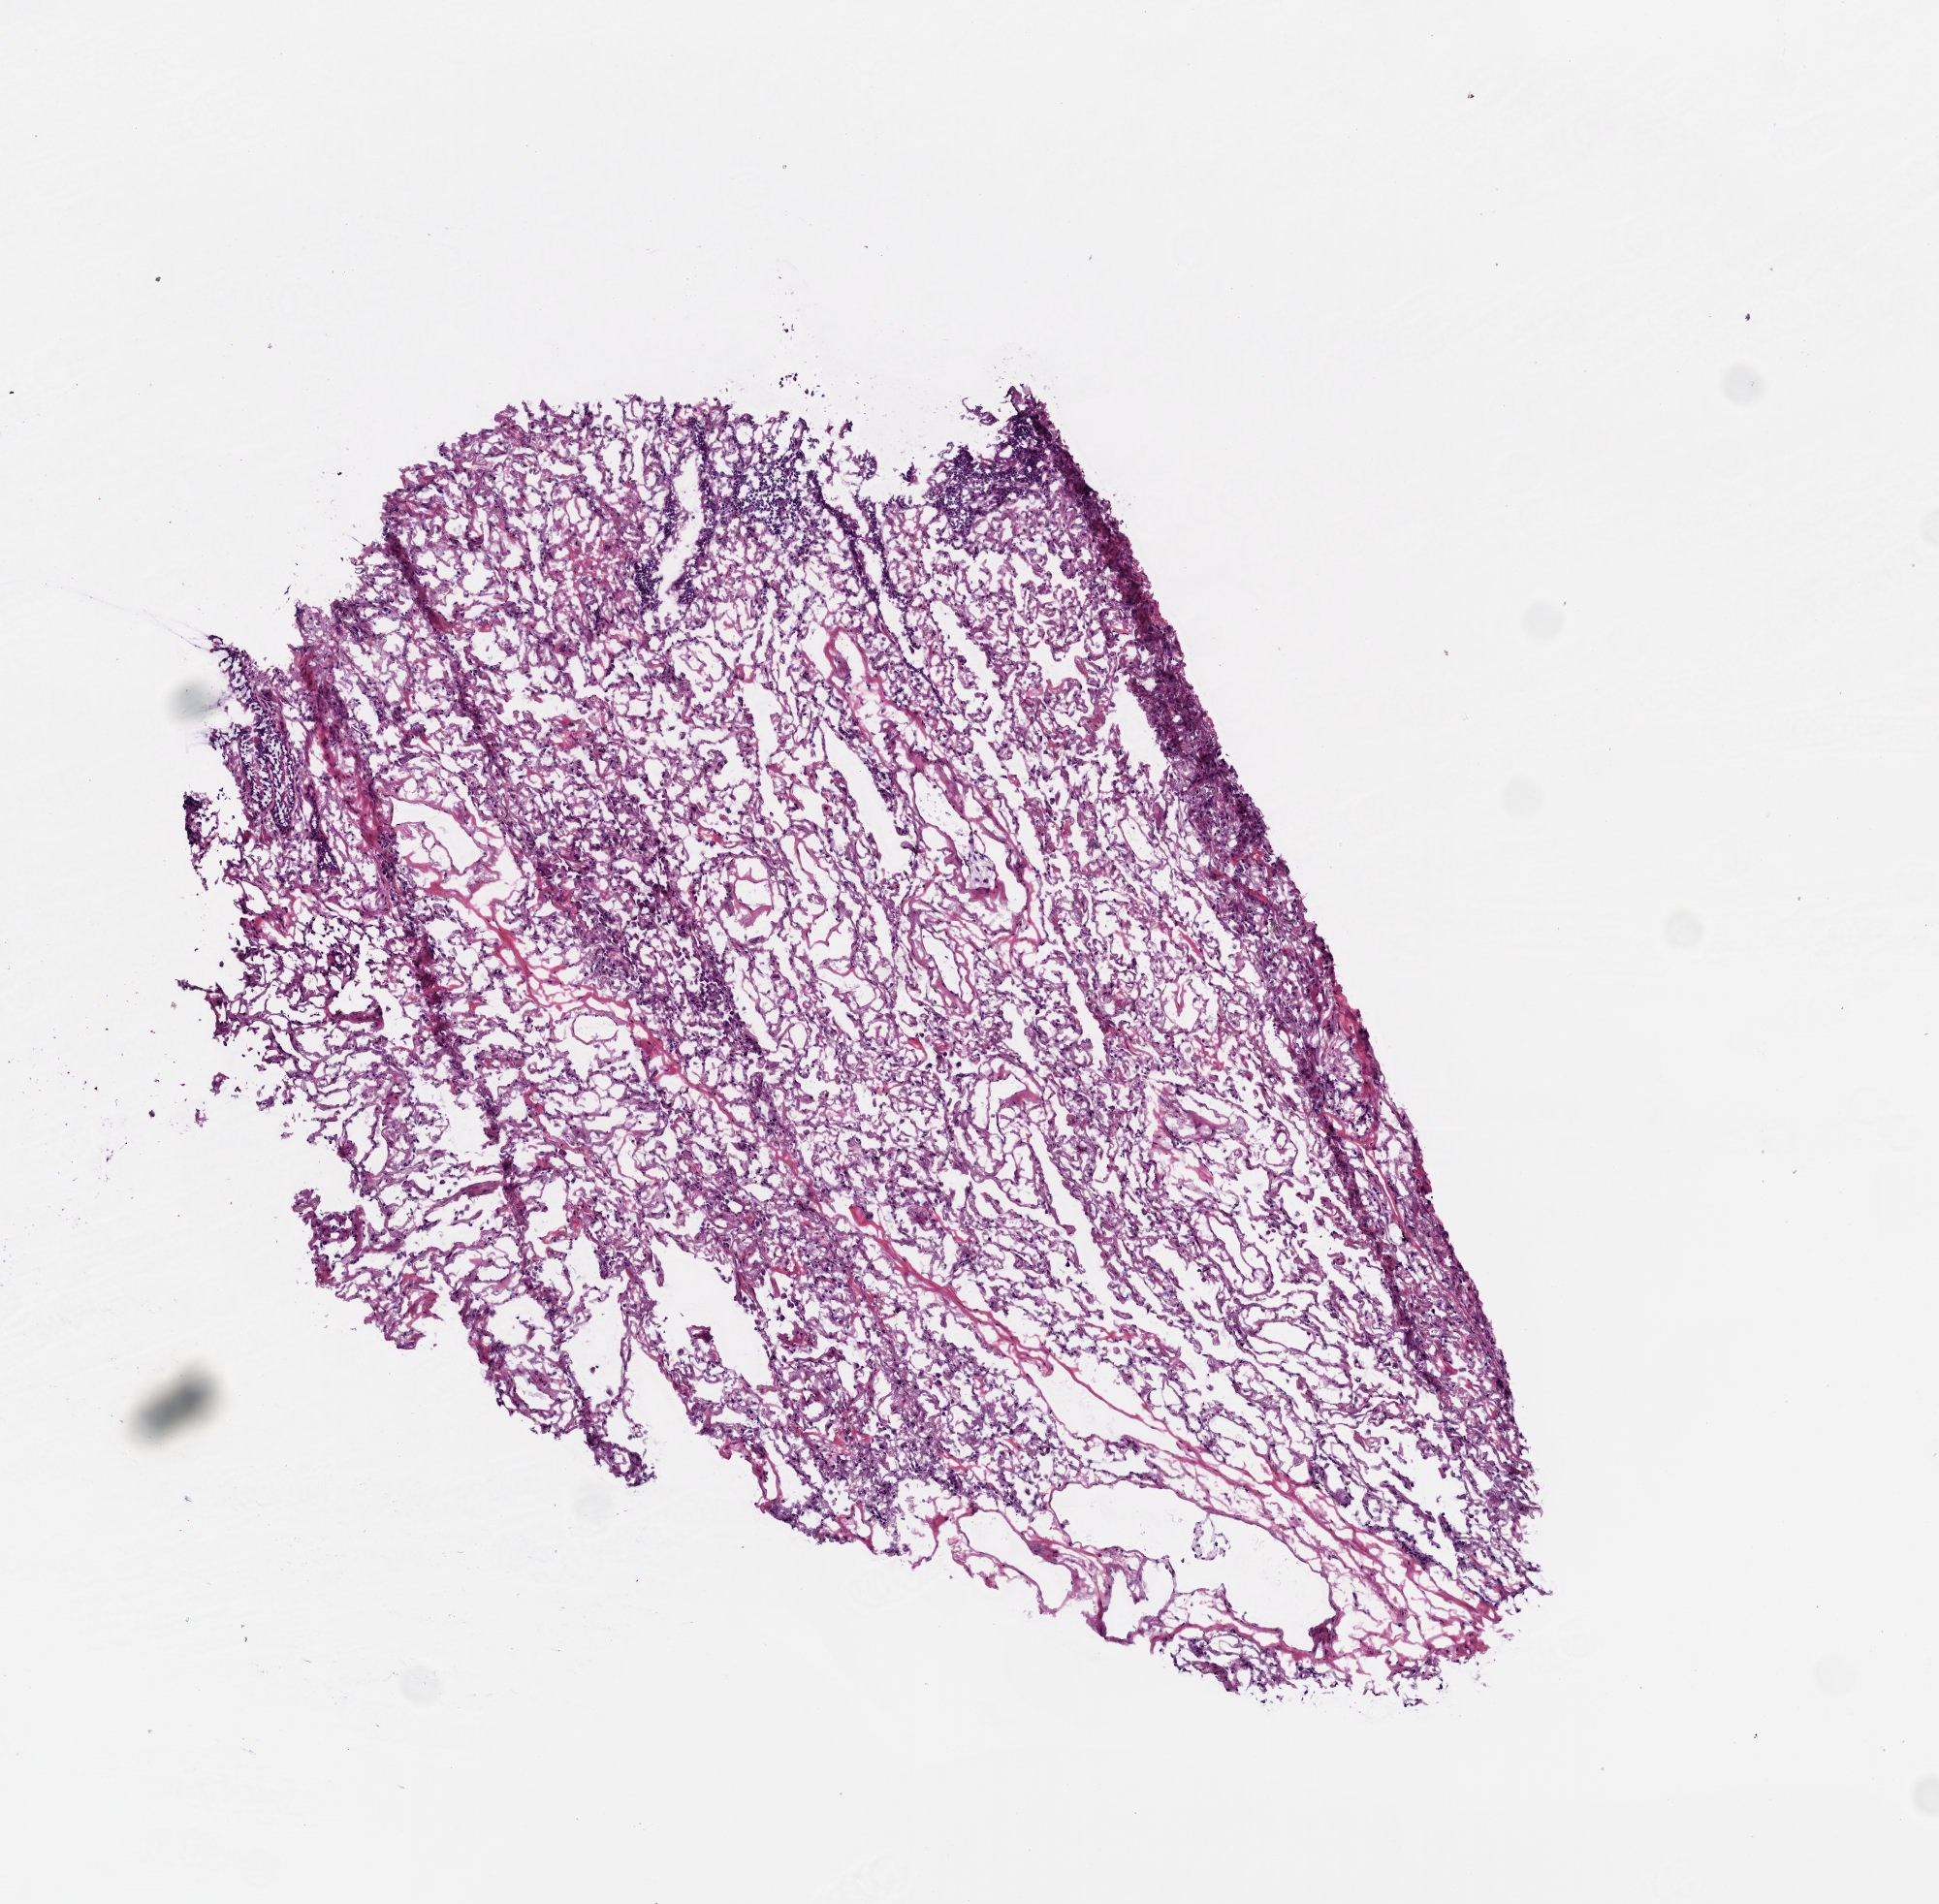
Digitized H&E-stained tissue section (whole slide) — whole scanned area (about 4.0 x 3.9 mm, slide scanned at 20x) shown as a low-resolution overview. Frozen section from the bottom of the tissue portion. Solid tissue normal (non-tumour tissue) sample from the lung. Female patient; age at initial diagnosis 69 years.
• this section: solid tissue normal sample (biorepository sample class)
• patient diagnosis: Squamous cell carcinoma, NOS (upper lobe, lung)